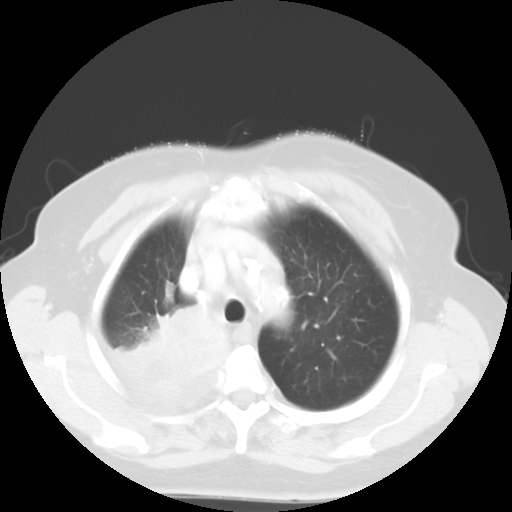
Chest CT, one axial slice; slice 43 of 52 in the series (ordered by position); reconstruction kernel STANDARD; lung window (W 1500 / L -600 HU); 5 mm slice thickness; 512 × 512 image matrix. Female patient, age 81 years. Case-level facts recorded for this patient, not image findings: clinical TNM (as recorded): T4 N3 M1b.
Outlined on this slice (bounding box drawn by a radiologist):
- lung tumour (recorded histology: adenocarcinoma): box from (x=97, y=304) to (x=233, y=396) px